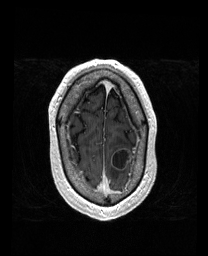
Brain MRI from a brain-tumour surgery series, one axial slice; position 151 of 192 along the scan axis; T1-weighted post-contrast; 1 mm slice thickness; 208 × 256 image matrix. From the clinical record (not read from this slice): histopathology: Metastatic Carcinoma from Lung Adenocarcinoma; tumour location: Left Frontal.
Structures marked on this image (expert manual segmentation):
- tumour: box from (x=113, y=148) to (x=132, y=169) px